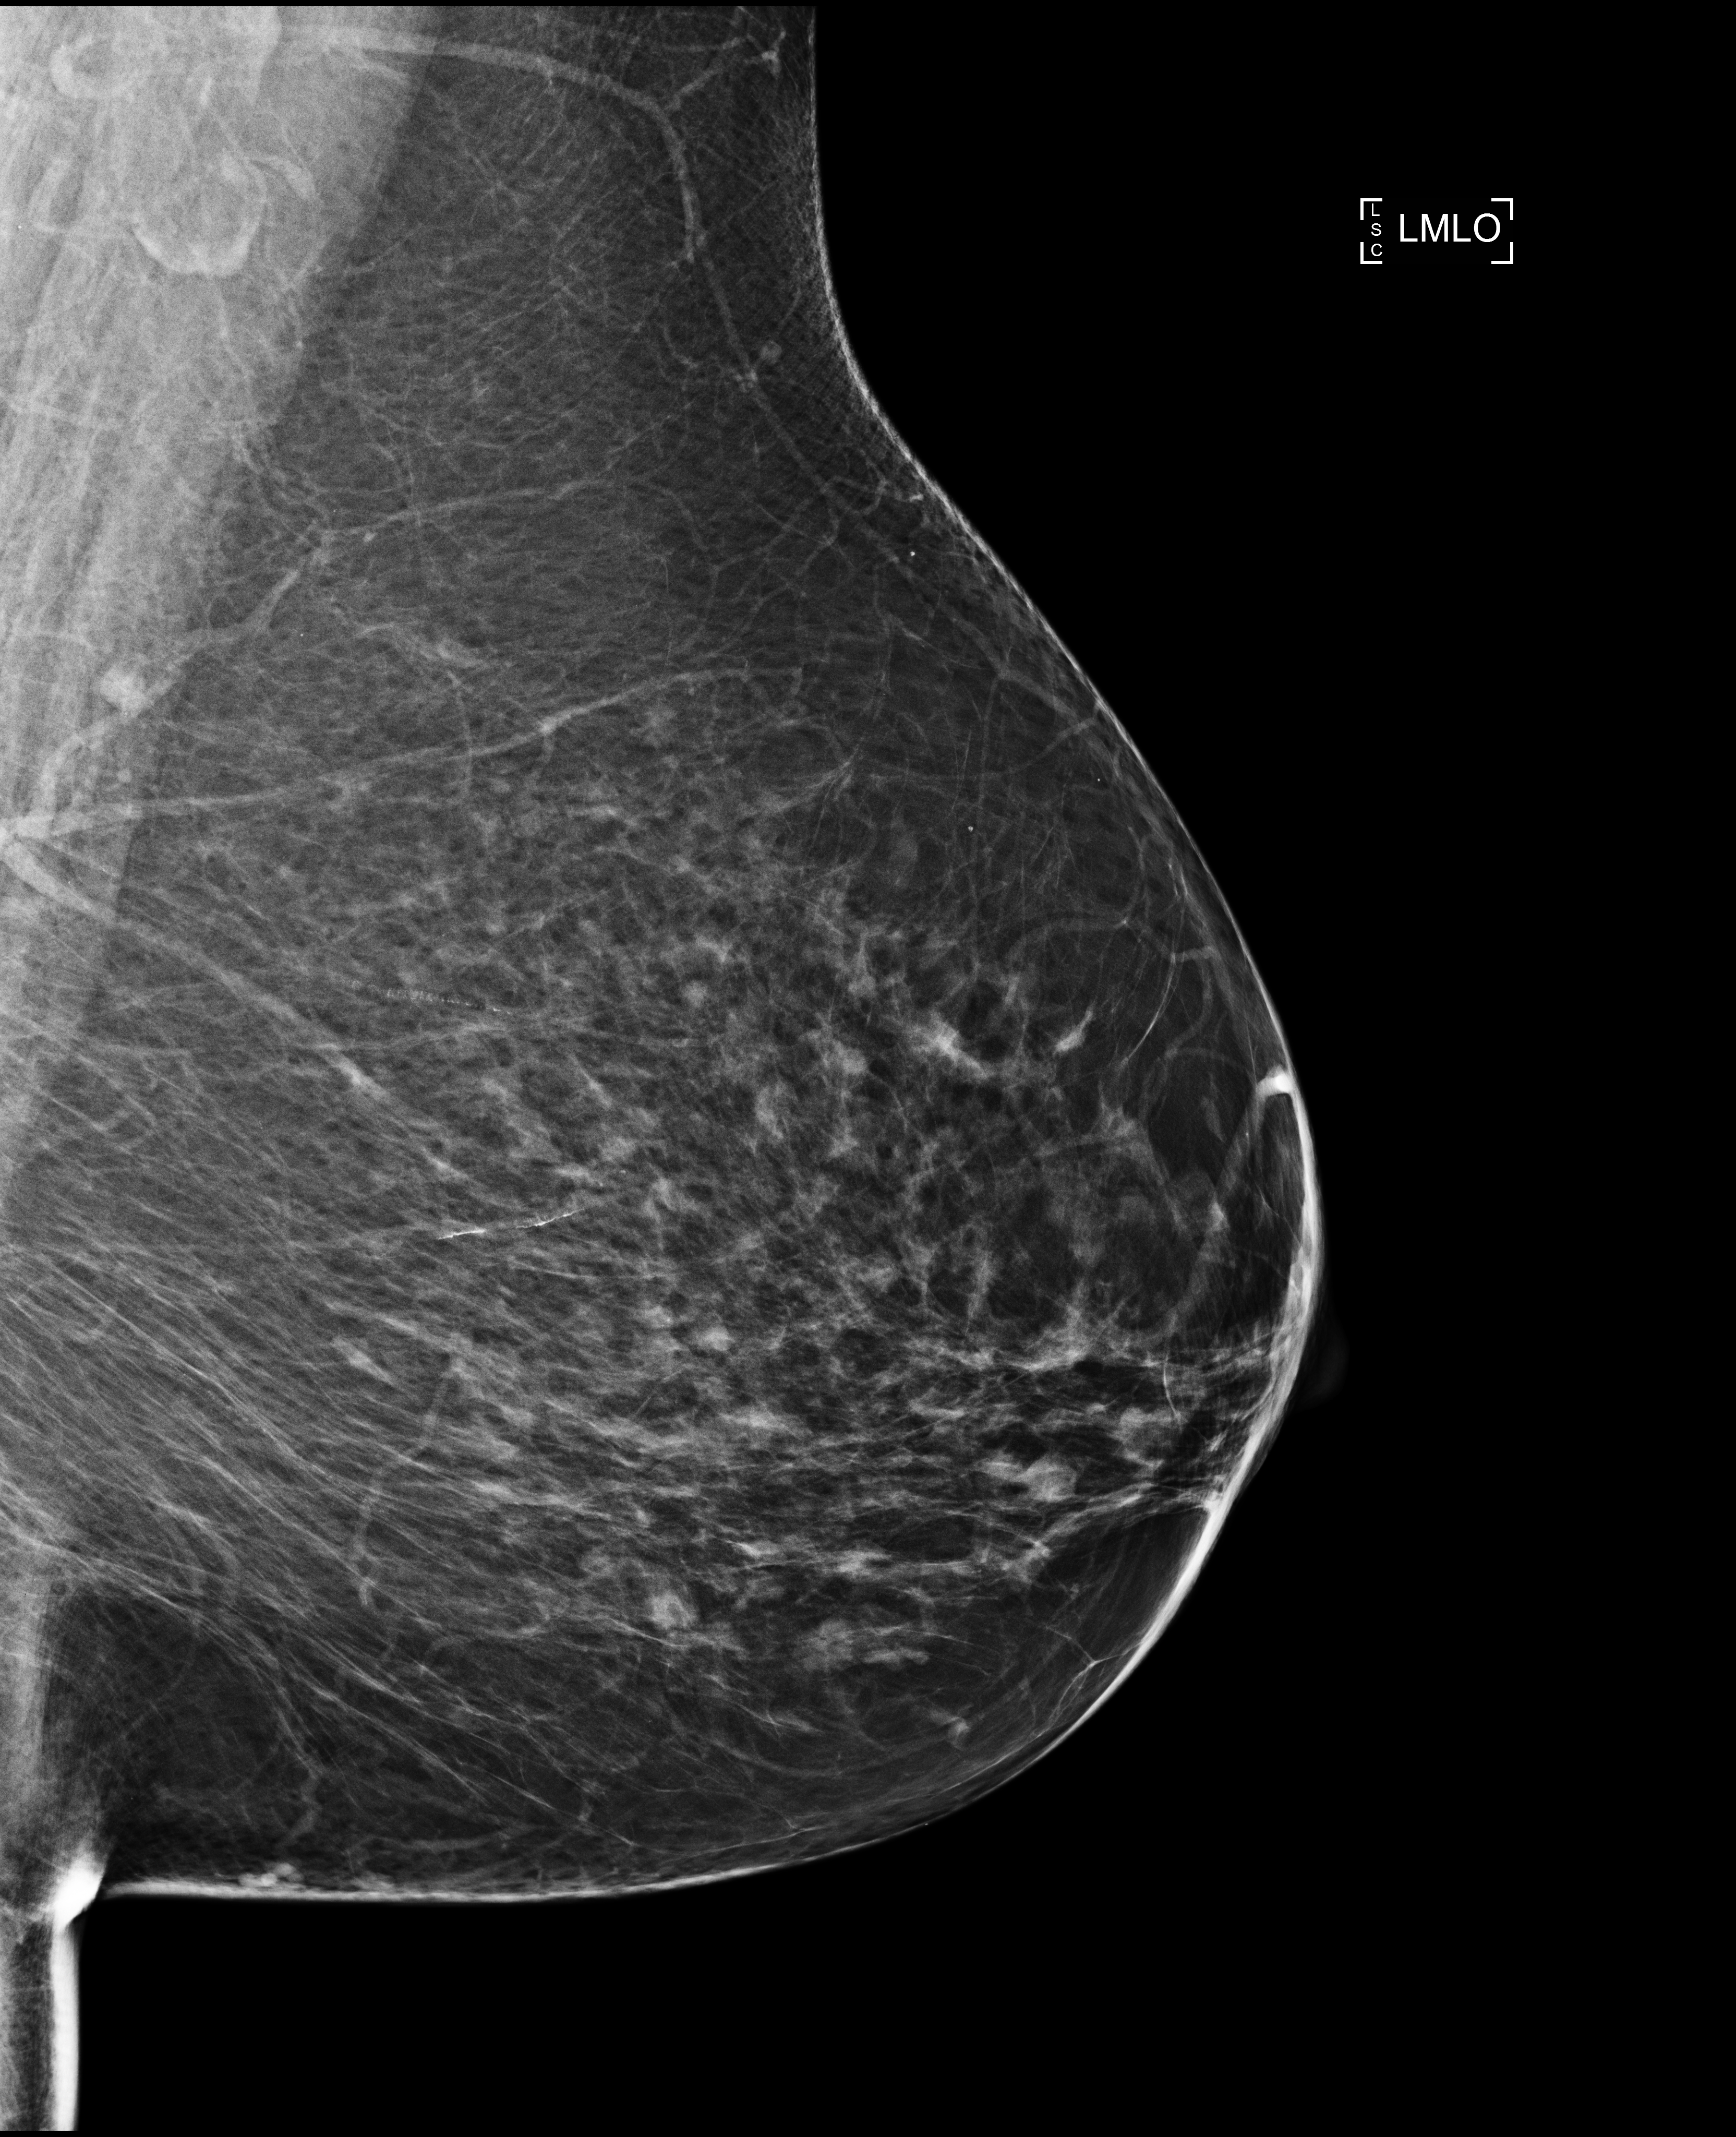
Full-field digital mammogram (FFDM), left breast, mediolateral oblique (MLO) view, annual screening mammography examination. Patient: female, 73 years.
- BI-RADS breast density category at the screening exam (both breasts, scale 1–4): 3
- final BI-RADS assessment for this screening round (tomosynthesis exam, both breasts): category 1
- recall: no recall after this screen